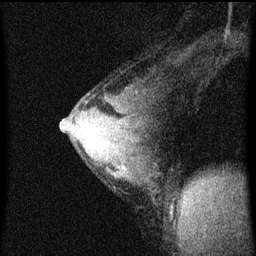
Breast MRI (dynamic contrast-enhanced), one sagittal slice. Slice 39 of 60 in the series (ordered by position). Dynamic contrast-enhanced series, image 2 of 4 at this slice position (ordered by acquisition). 1.5 T. TE 4.2 ms, TR 8 ms. 2 mm slice thickness. 256 × 256 image matrix, field of view 180 × 180 mm. Female patient, age 33 years.
Structures marked on this image (semi-automatically segmented with operator editing):
- analysis volume of interest (the breast-tissue region the enhancement analysis was run in; not a lesion): box from (x=61, y=78) to (x=169, y=207) px
- tumour enhancement mask (voxels above the 70 % enhancement threshold inside the analysis volume of interest): (x=61, y=122)–(x=87, y=151)